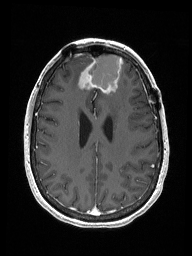
Brain MRI from a brain-tumour surgery series, one axial slice; slice 62 of 192 in the series (ordered by position); T1-weighted post-contrast; 1 mm slice thickness; 192 × 256 image matrix. Case-level facts recorded for this patient, not image findings: histopathology: Metastastic Carcinoma from Breast primary.
Annotated regions visible in this slice (expert manual segmentation):
- previous resection cavity: bounding box [x1, y1, x2, y2] px = [88, 54, 123, 91]